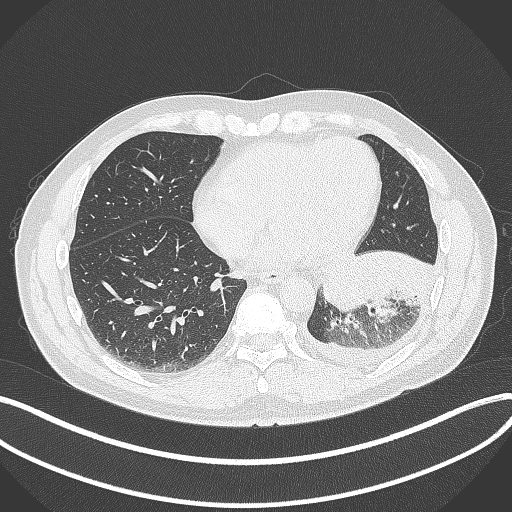
Chest CT, one axial slice; slice 119 of 342 in the series (ordered by position); lung window (W 1500 / L -600 HU); 512 × 512 image matrix, field of view 400 × 400 mm. Patient: male, 58 years. Case-level facts recorded for this patient, not image findings: clinical TNM (as recorded): T3 N1 M1b; histopathological grade: G3.
Outlined on this slice (bounding box drawn by a radiologist):
- lung tumour (recorded histology: small cell carcinoma): bounding box (x1, y1, x2, y2) in pixels: (324, 247, 436, 314)